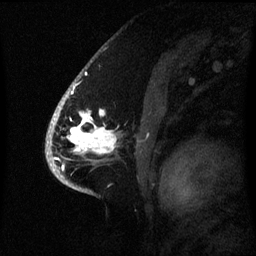
Breast MRI (dynamic contrast-enhanced), one sagittal slice; position 45 of 60 along the scan axis; dynamic contrast-enhanced series, image 2 of 3 at this slice position (ordered by acquisition); 1.5 T; TE 4.2 ms, TR 8.4 ms; 2.1 mm slice thickness; 256 × 256 image matrix, field of view 220 × 220 mm. Patient: female, 53 years. Case-level facts recorded for this patient, not image findings: setting: breast cancer imaged before/during neoadjuvant chemotherapy; receptor status: HR-positive, HER2-negative.
Outlined on this slice (semi-automatically segmented with operator editing):
- analysis volume of interest (the breast-tissue region the enhancement analysis was run in; not a lesion): bounding box [x1, y1, x2, y2] px = [52, 90, 123, 171]
- tumour enhancement mask (voxels above the 70 % enhancement threshold inside the analysis volume of interest): [53, 92, 116, 161]